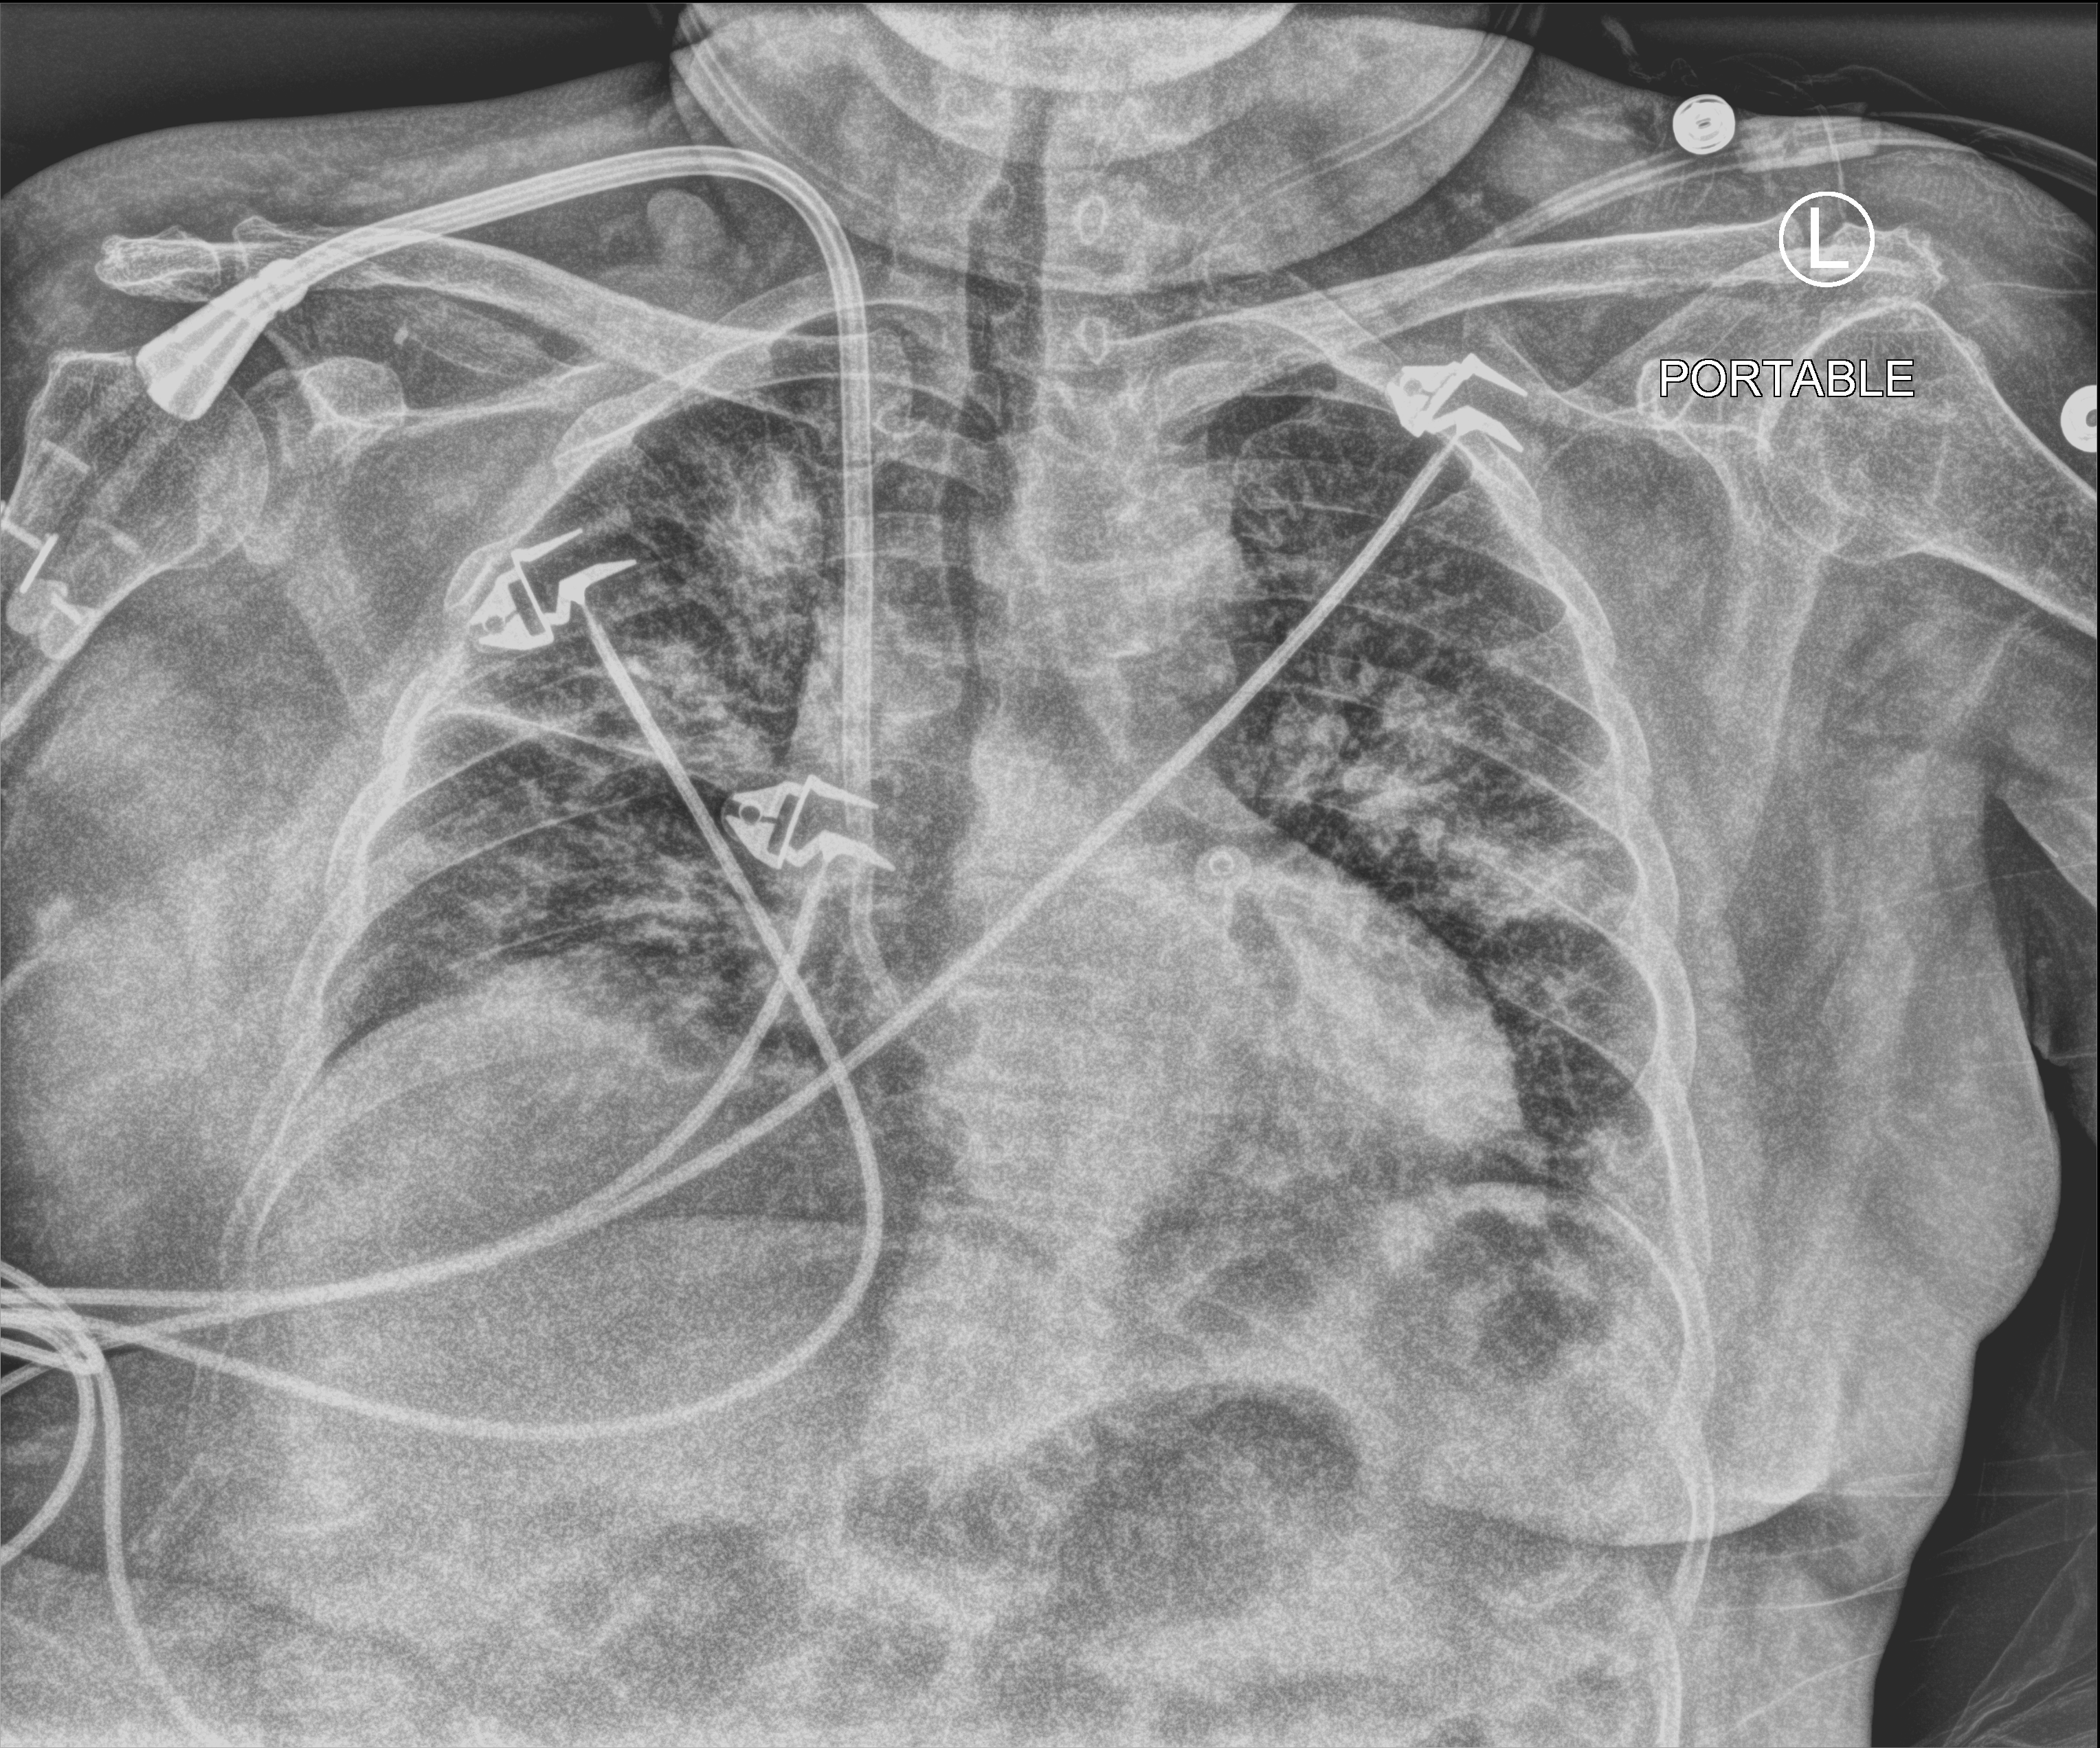
Bedside chest radiograph (computed radiography), anteroposterior (AP) projection. Female patient hospitalised with COVID-19, age 60–74 years.
Admission-level facts for this patient (not findings on this image; timing relative to this image not recorded): hypertension (admission record): yes; admitted to intensive care during this hospital stay: no; length of hospital stay: 5 days.